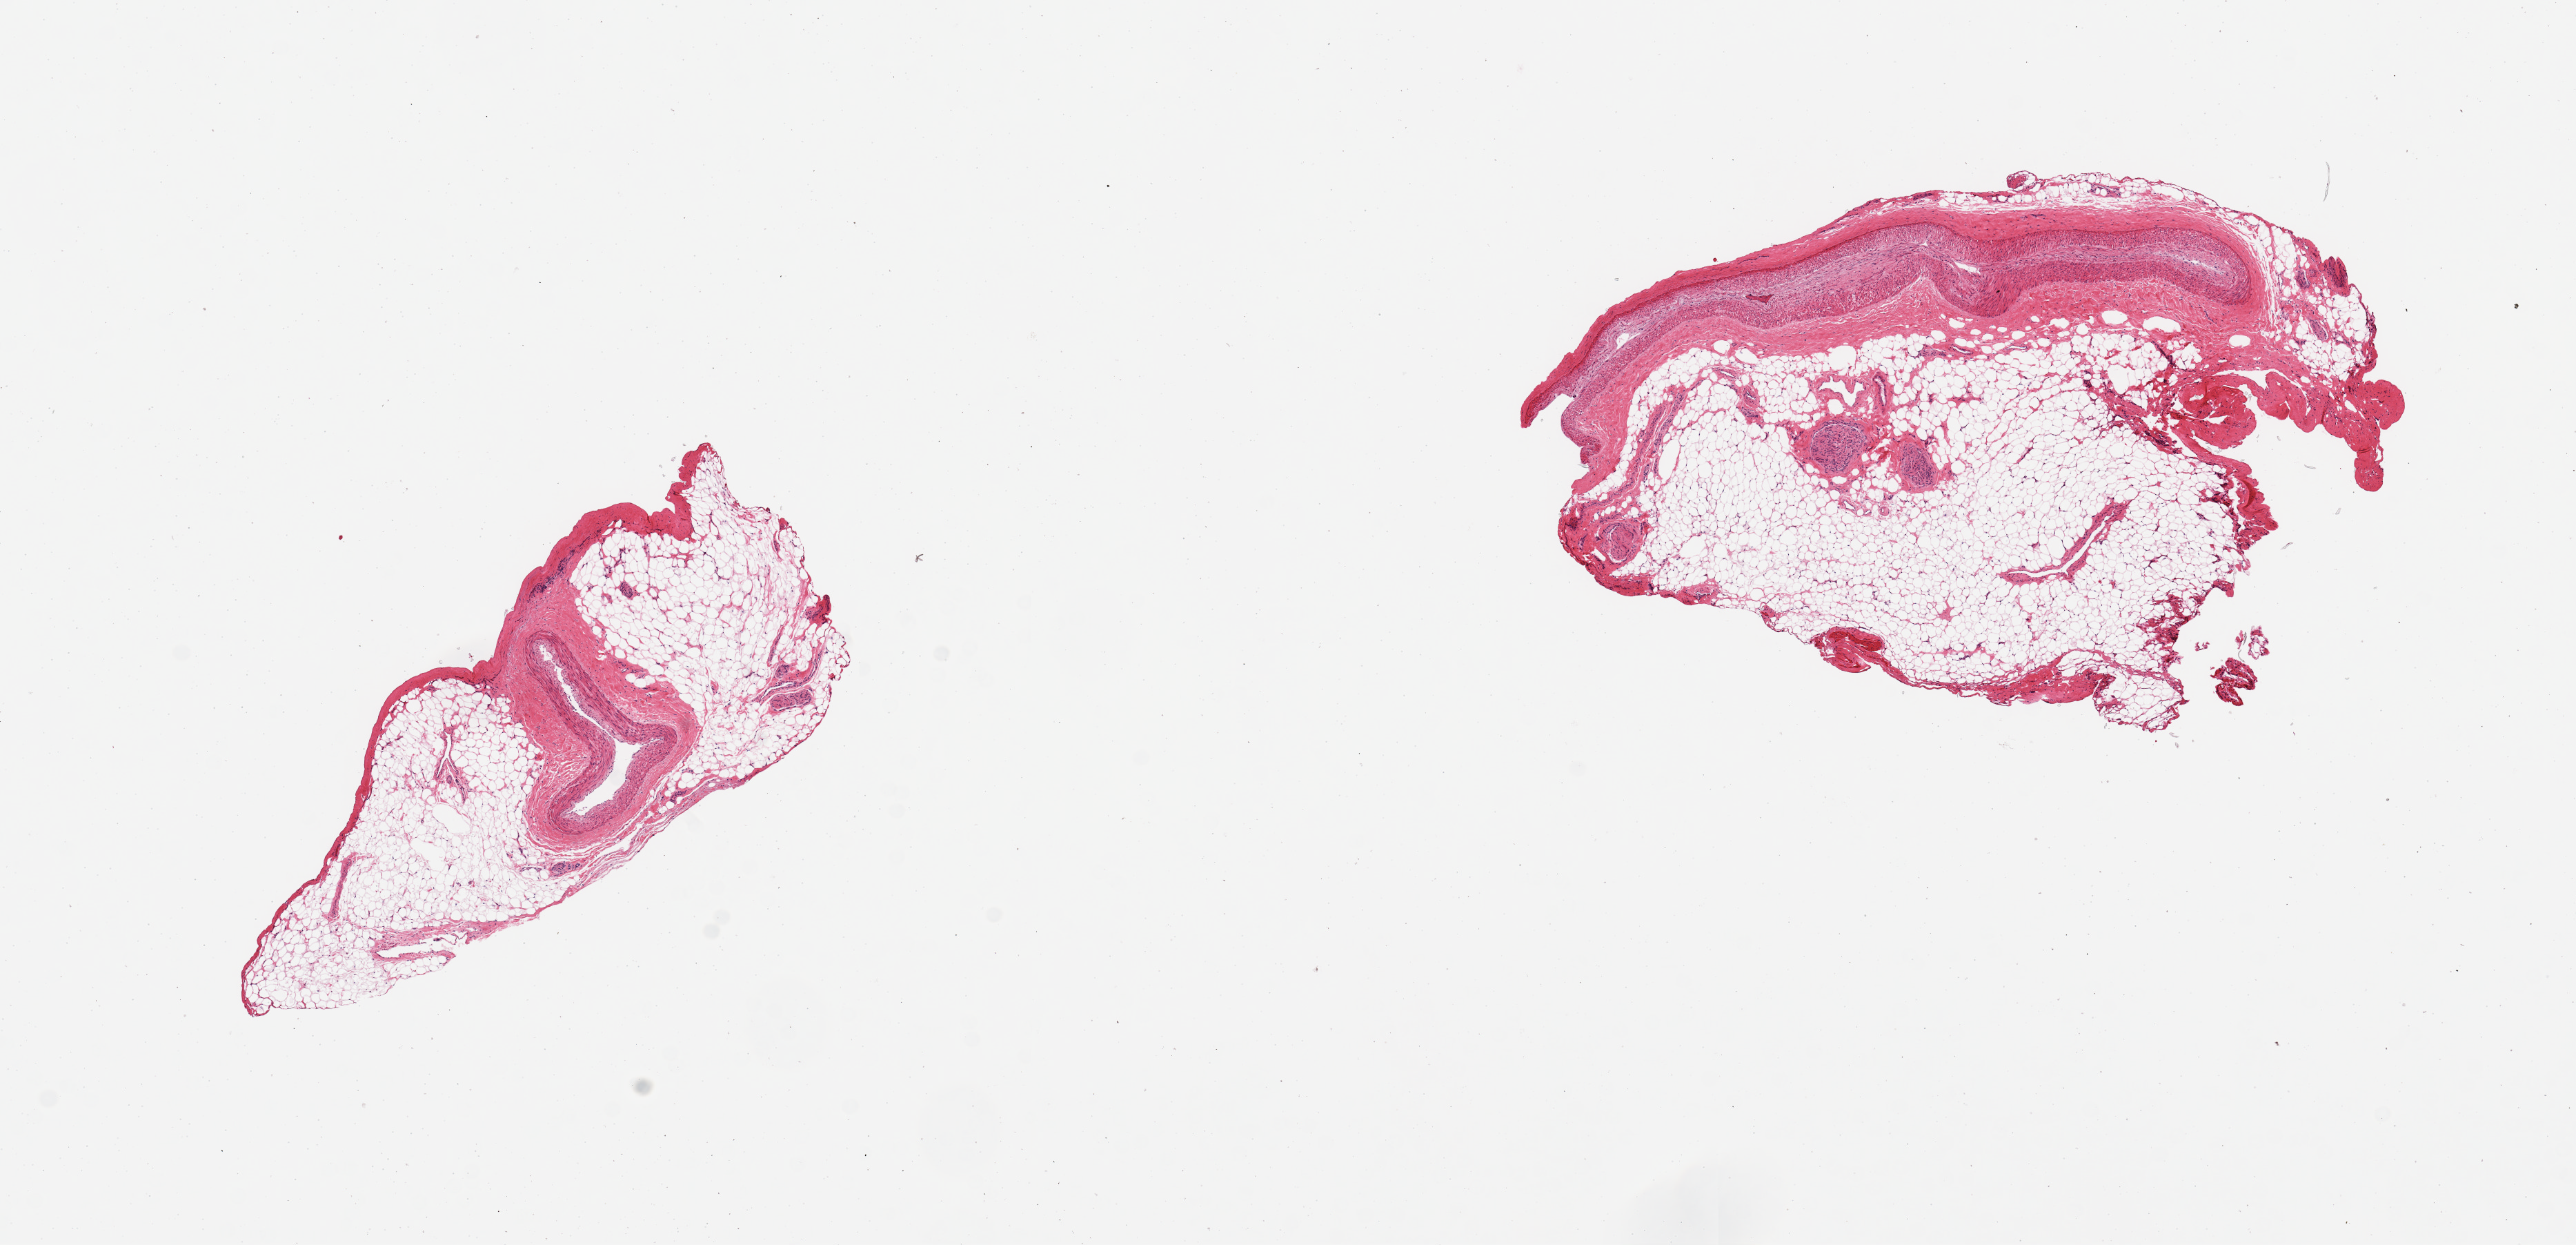
Whole-slide image, haematoxylin and eosin stain — a low-resolution overview of the entire scanned area, about 14.8 x 7.1 mm (slide scanned at 20x). PAXgene-fixed paraffin-embedded (PFPE) section. Section of coronary artery (target tissue). Donor tissue sample. Donor sex: female.
- pathologist's review note for this sample: 2 pieces; no lesions, ~80% is attached fat/nerve